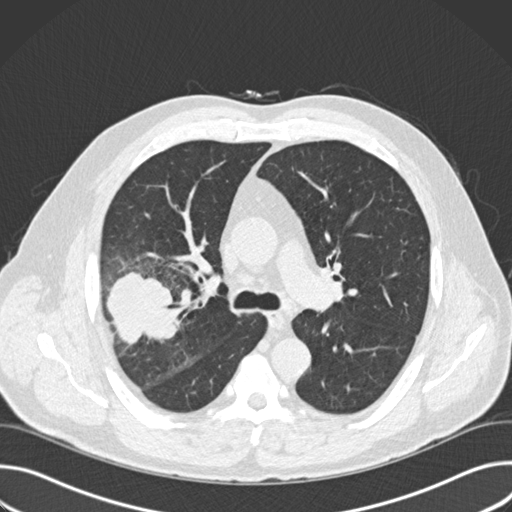
Low-dose screening chest CT, one axial slice; slice 104 of 157 in the series (ordered by position); 120 kVp; lung window (W 1500 / L -600 HU); 2 mm slice thickness; 512 × 512 image matrix, field of view 380 × 380 mm.
Outlined on this slice (outlined manually by an expert reader):
- lesion 1 (tumor, upper lobe of right lung): bounding box <107,272,182,344> (left, top, right, bottom; pixels)